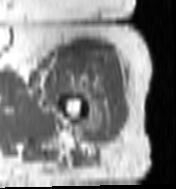
MRI of an extremity soft-tissue mass, one axial slice. MR volume resampled by the dataset authors to the PET/CT grid (not the native acquisition matrix). 3.27 mm slice thickness. 176 × 189 image matrix, field of view 172 × 185 mm. Female patient. From the clinical record (not read from this slice): histological type: undifferentiated – high grade; grade: high; site of the primary tumour: left thigh.
Annotated regions visible in this slice (expert contour drawn on MRI and transferred to this co-registered scan by the dataset authors):
- gross tumour volume including surrounding oedema: box from (x=73, y=75) to (x=113, y=143) px
- gross tumour volume (mass): (x=82, y=112)–(x=109, y=136)